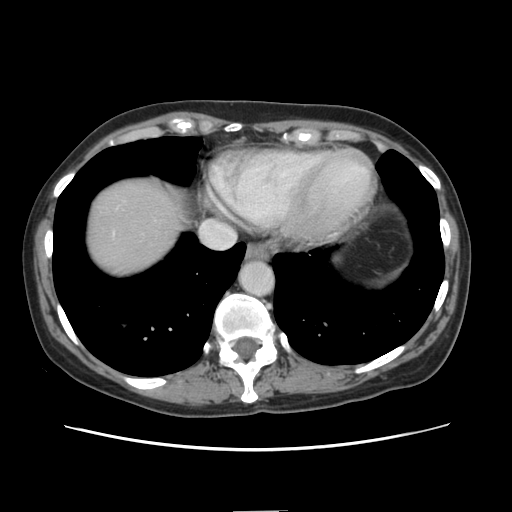
Contrast-enhanced abdominal CT, one axial slice; position 129 of 141 along the scan axis; soft-tissue window (W 400 / L 40 HU); 2.5 mm slice thickness; 512 × 512 image matrix, field of view 350 × 350 mm. Female patient, age 63 years. From the clinical record (not read from this slice): diagnosis: colorectal cancer liver metastases, imaged before liver resection; multiple liver metastases: yes; largest metastasis: 3.2 cm; disease in both lobes: yes.
Annotated regions visible in this slice (outlined manually by an expert reader):
- liver: bounding box <86,176,184,277> (left, top, right, bottom; pixels)